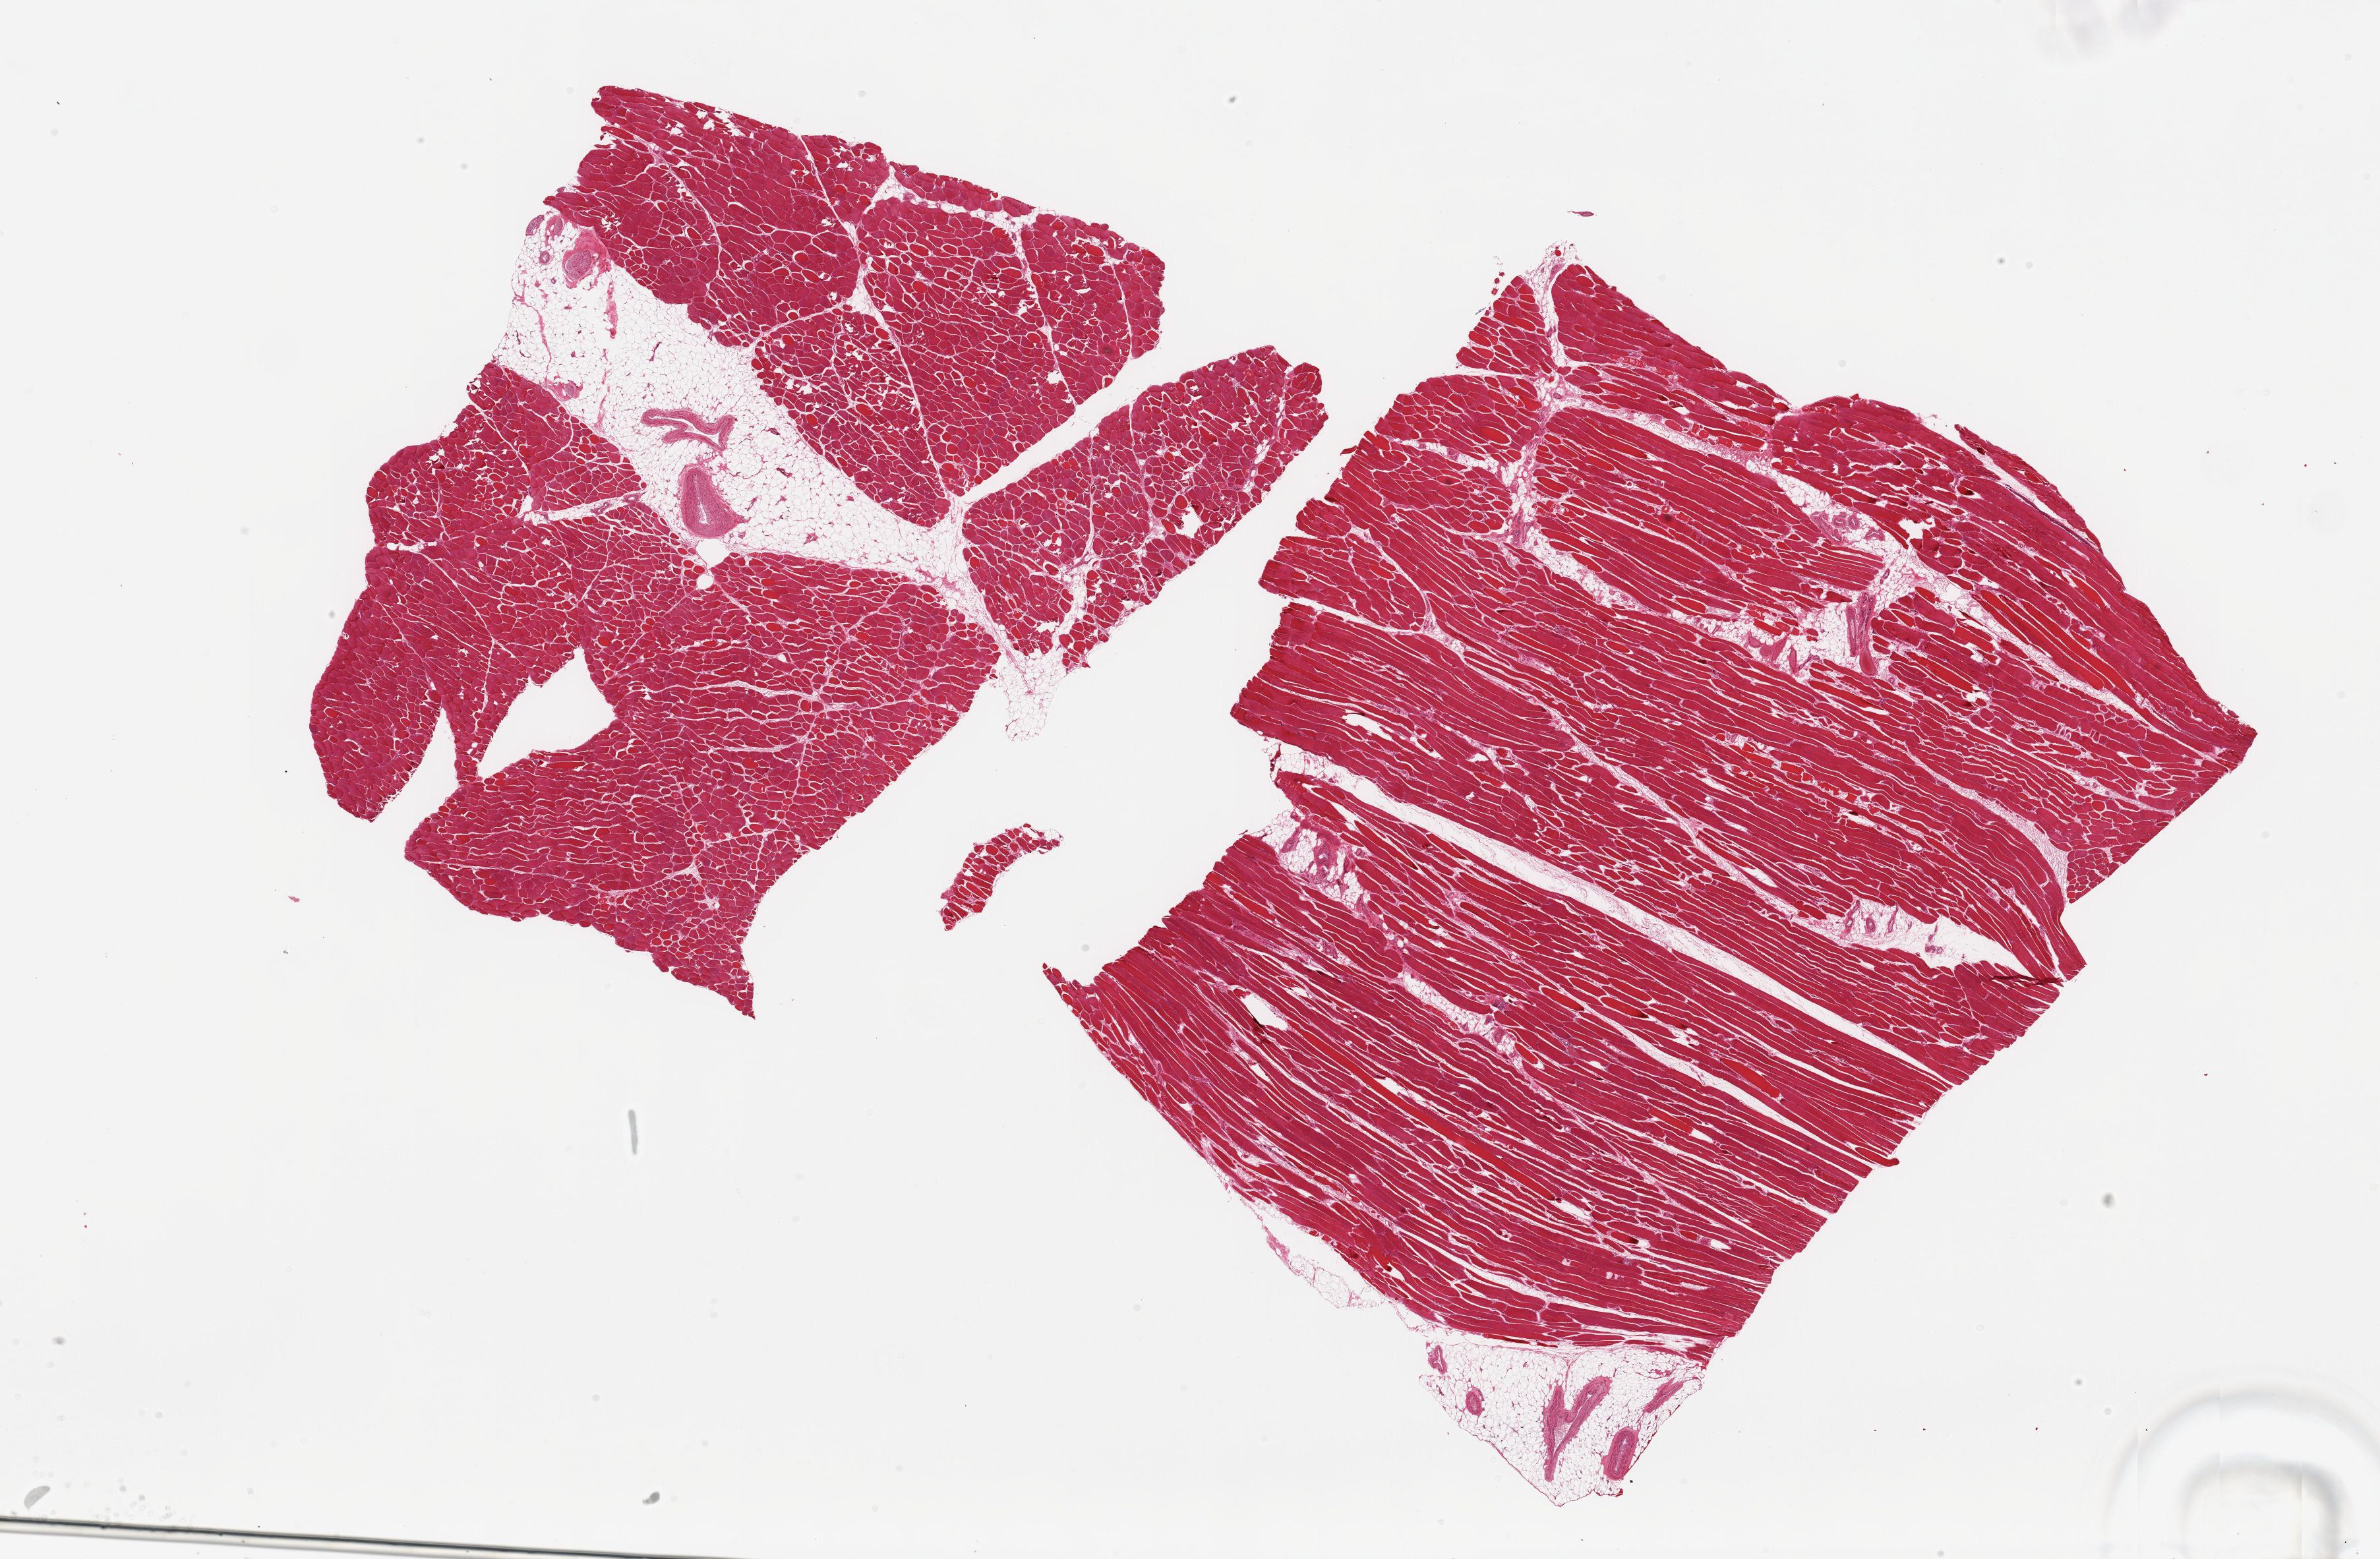
Whole-slide image, haematoxylin and eosin stain, shown as a low-resolution overview of the whole scanned area (about 28.5 x 18.7 mm), PAXgene-fixed paraffin-embedded (PFPE) section, target tissue: skeletal muscle, tissue donor sample. Donor: male.
Review note (as recorded): 2 pieces, interstitial/ahderent fat is ~15%.